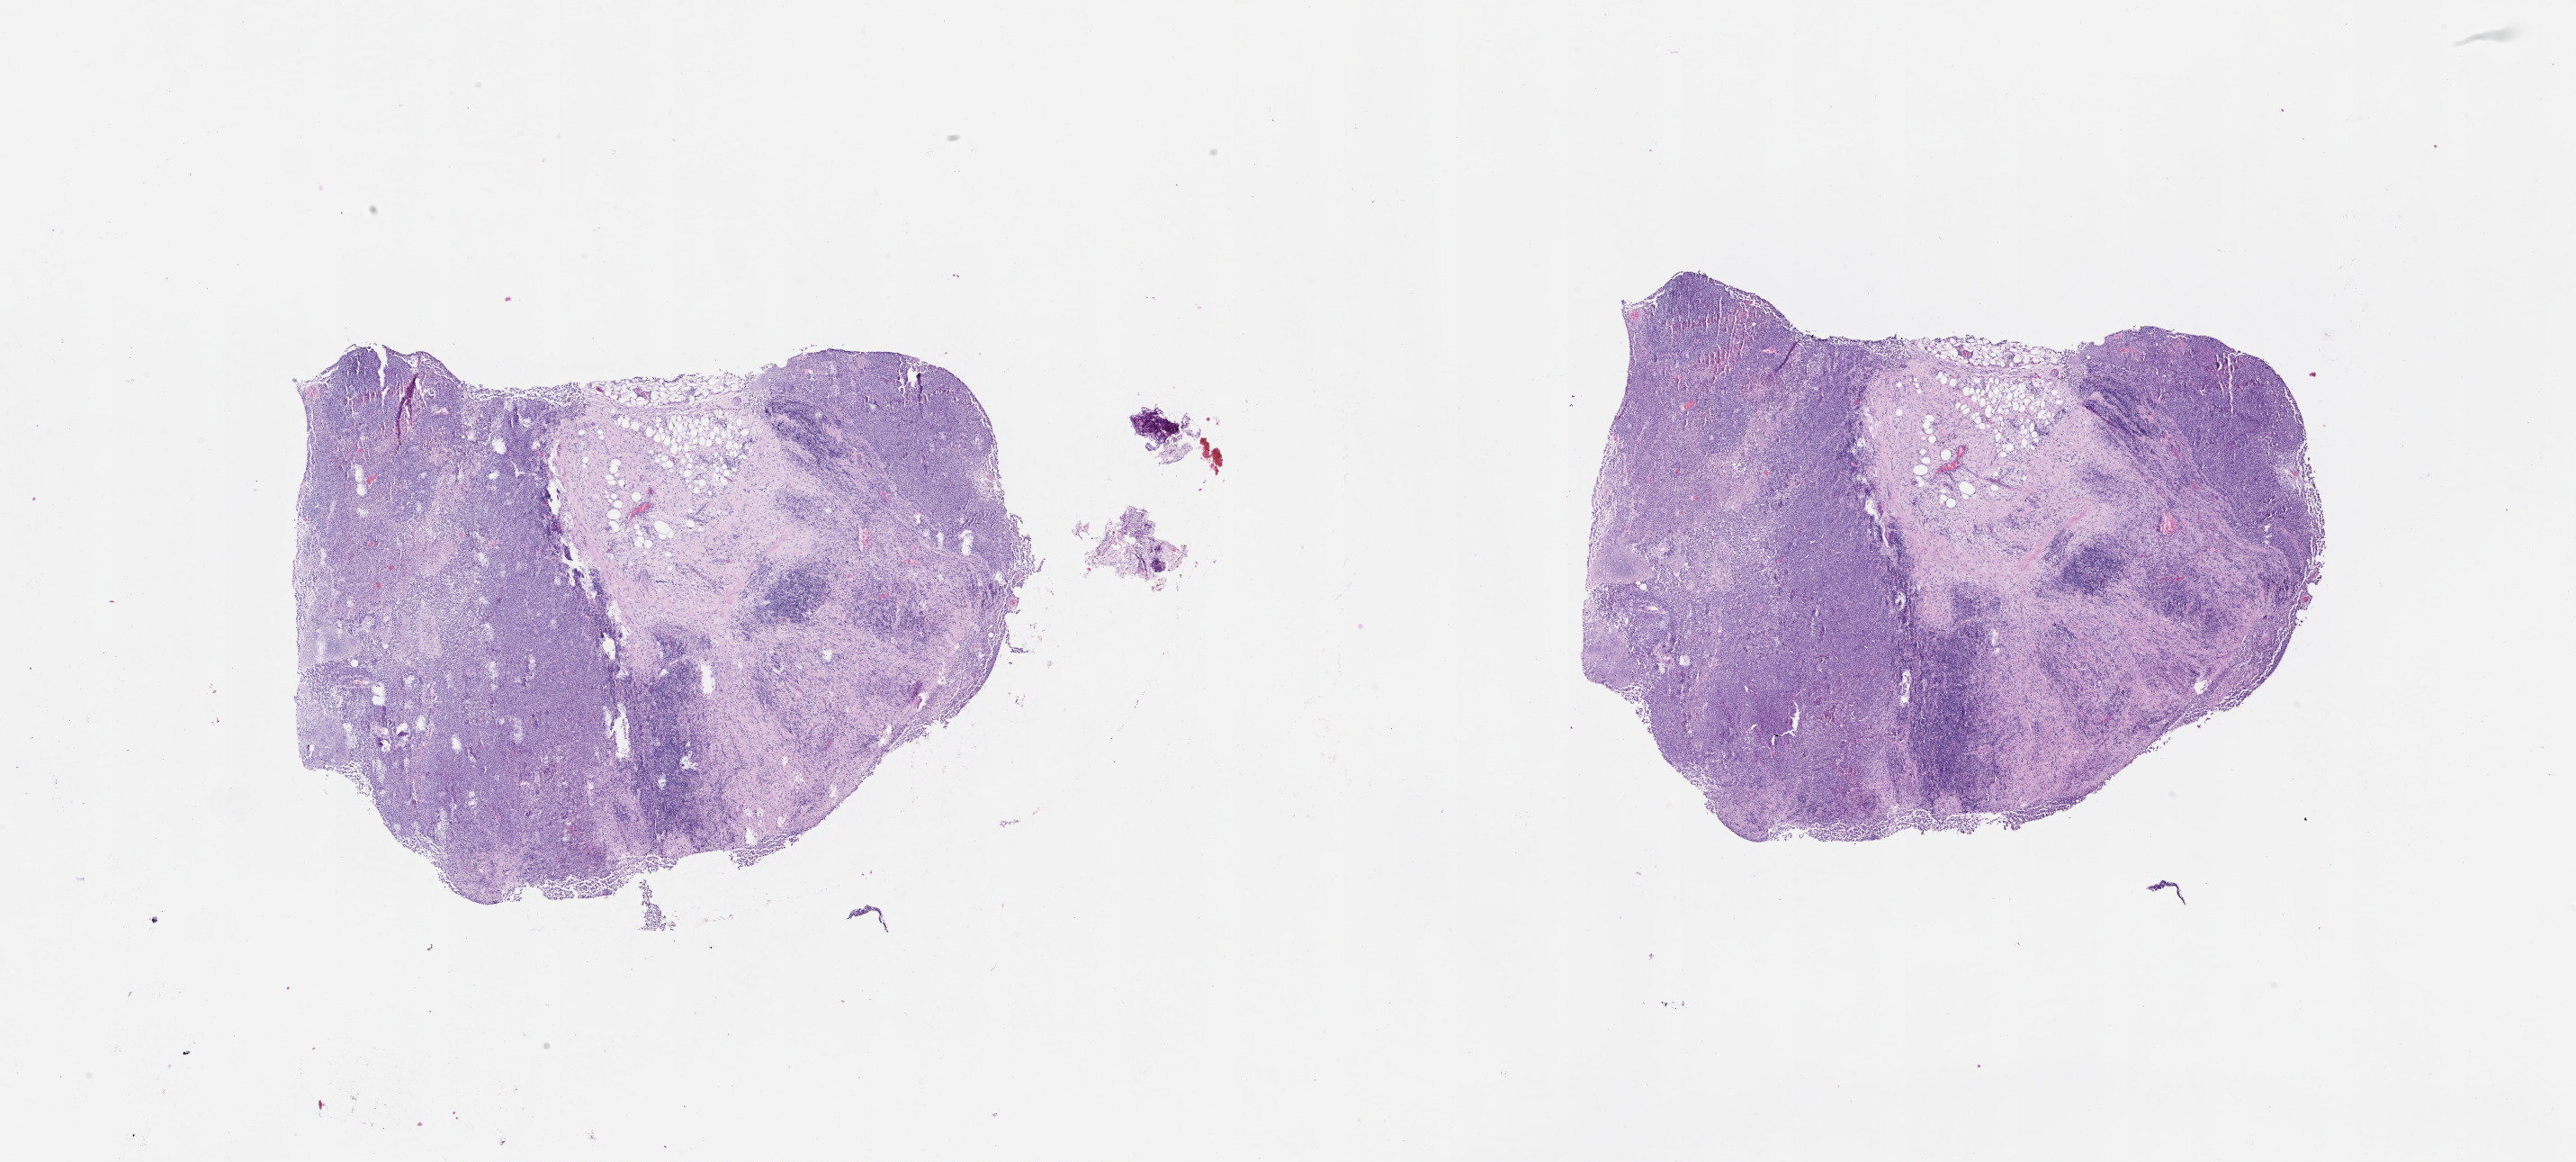
Digitized H&E tissue section (whole slide) — a low-resolution overview of the entire scanned area, about 23.1 x 10.4 mm (acquisition: 20x scan). Male, 72 y/o.
Patient diagnosis: Malignant melanoma, NOS.